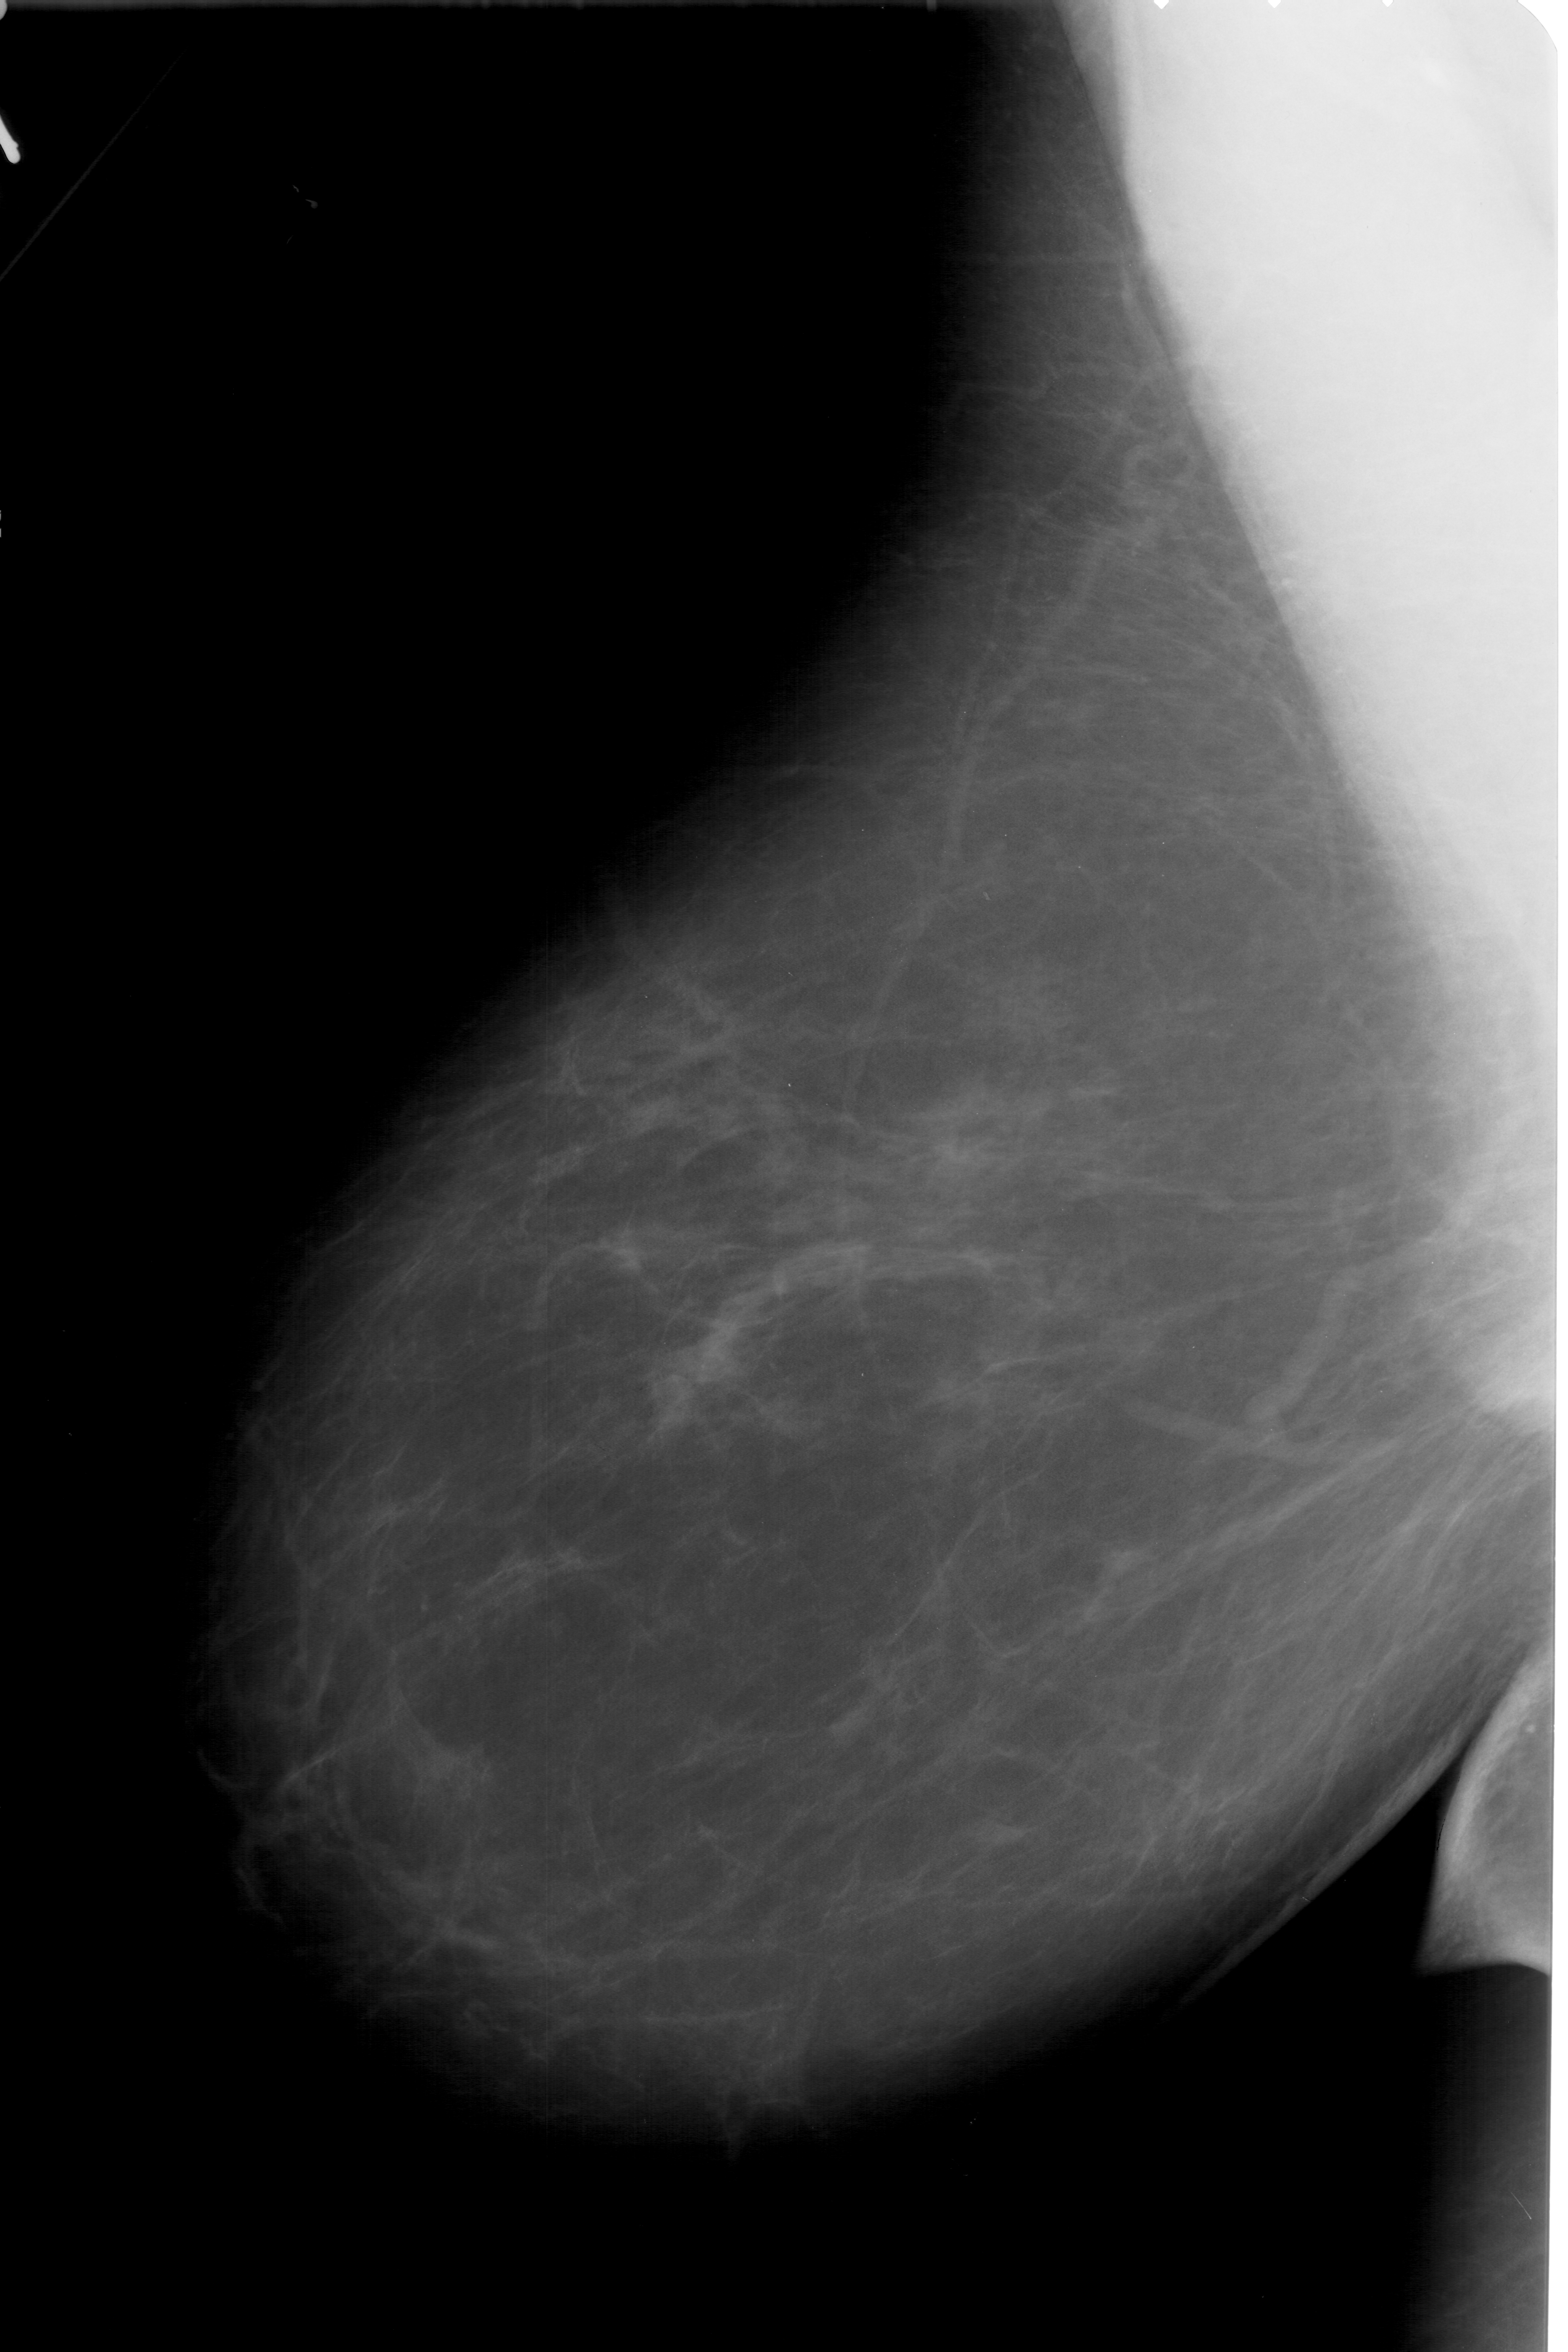
Mammogram (digitized film); left breast; mediolateral oblique (MLO) view; 1568 × 2352 image matrix.
Marked abnormalities (boxes around the expert regions of interest):
- calcifications, morphology pleomorphic, distribution clustered; BI-RADS assessment category 4; subtlety rating 1 on a 1 (subtle) to 5 (obvious) scale; pathology (as recorded): malignant: bounding box [x1, y1, x2, y2] px = [640, 1310, 742, 1449]